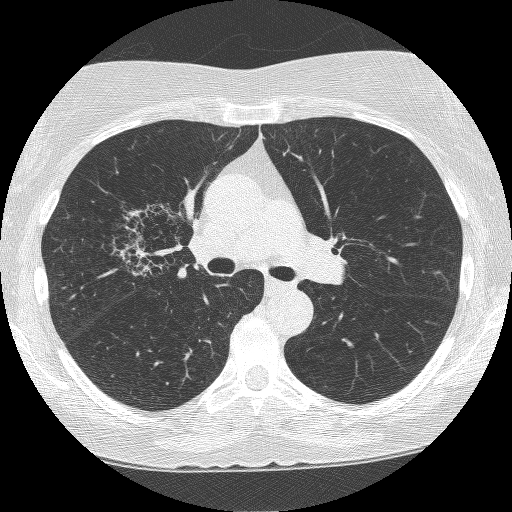
Low-dose screening chest CT, axial slice. Second screening round (one year after baseline). Lung window (W 1500 / L -600 HU). Slice 151 of 249 in the series. 512 × 512 image matrix, field of view 308 × 308 mm. Female, age 64 years at enrolment. Former smoker at enrolment.
Lesion marked by an expert reader, bounding box (x1, y1, x2, y2) in pixels: (116, 205, 205, 290). The screening reader recorded 4 non-calcified nodules or masses ≥4 mm on this exam; which of them this box marks is not recorded. Lung cancer was diagnosed 381 days after this screen (after the third annual screen): adenocarcinoma, NOS, right upper lobe, right middle lobe, right hilum, stage IV (AJCC 6th edition), 85 mm at pathology.